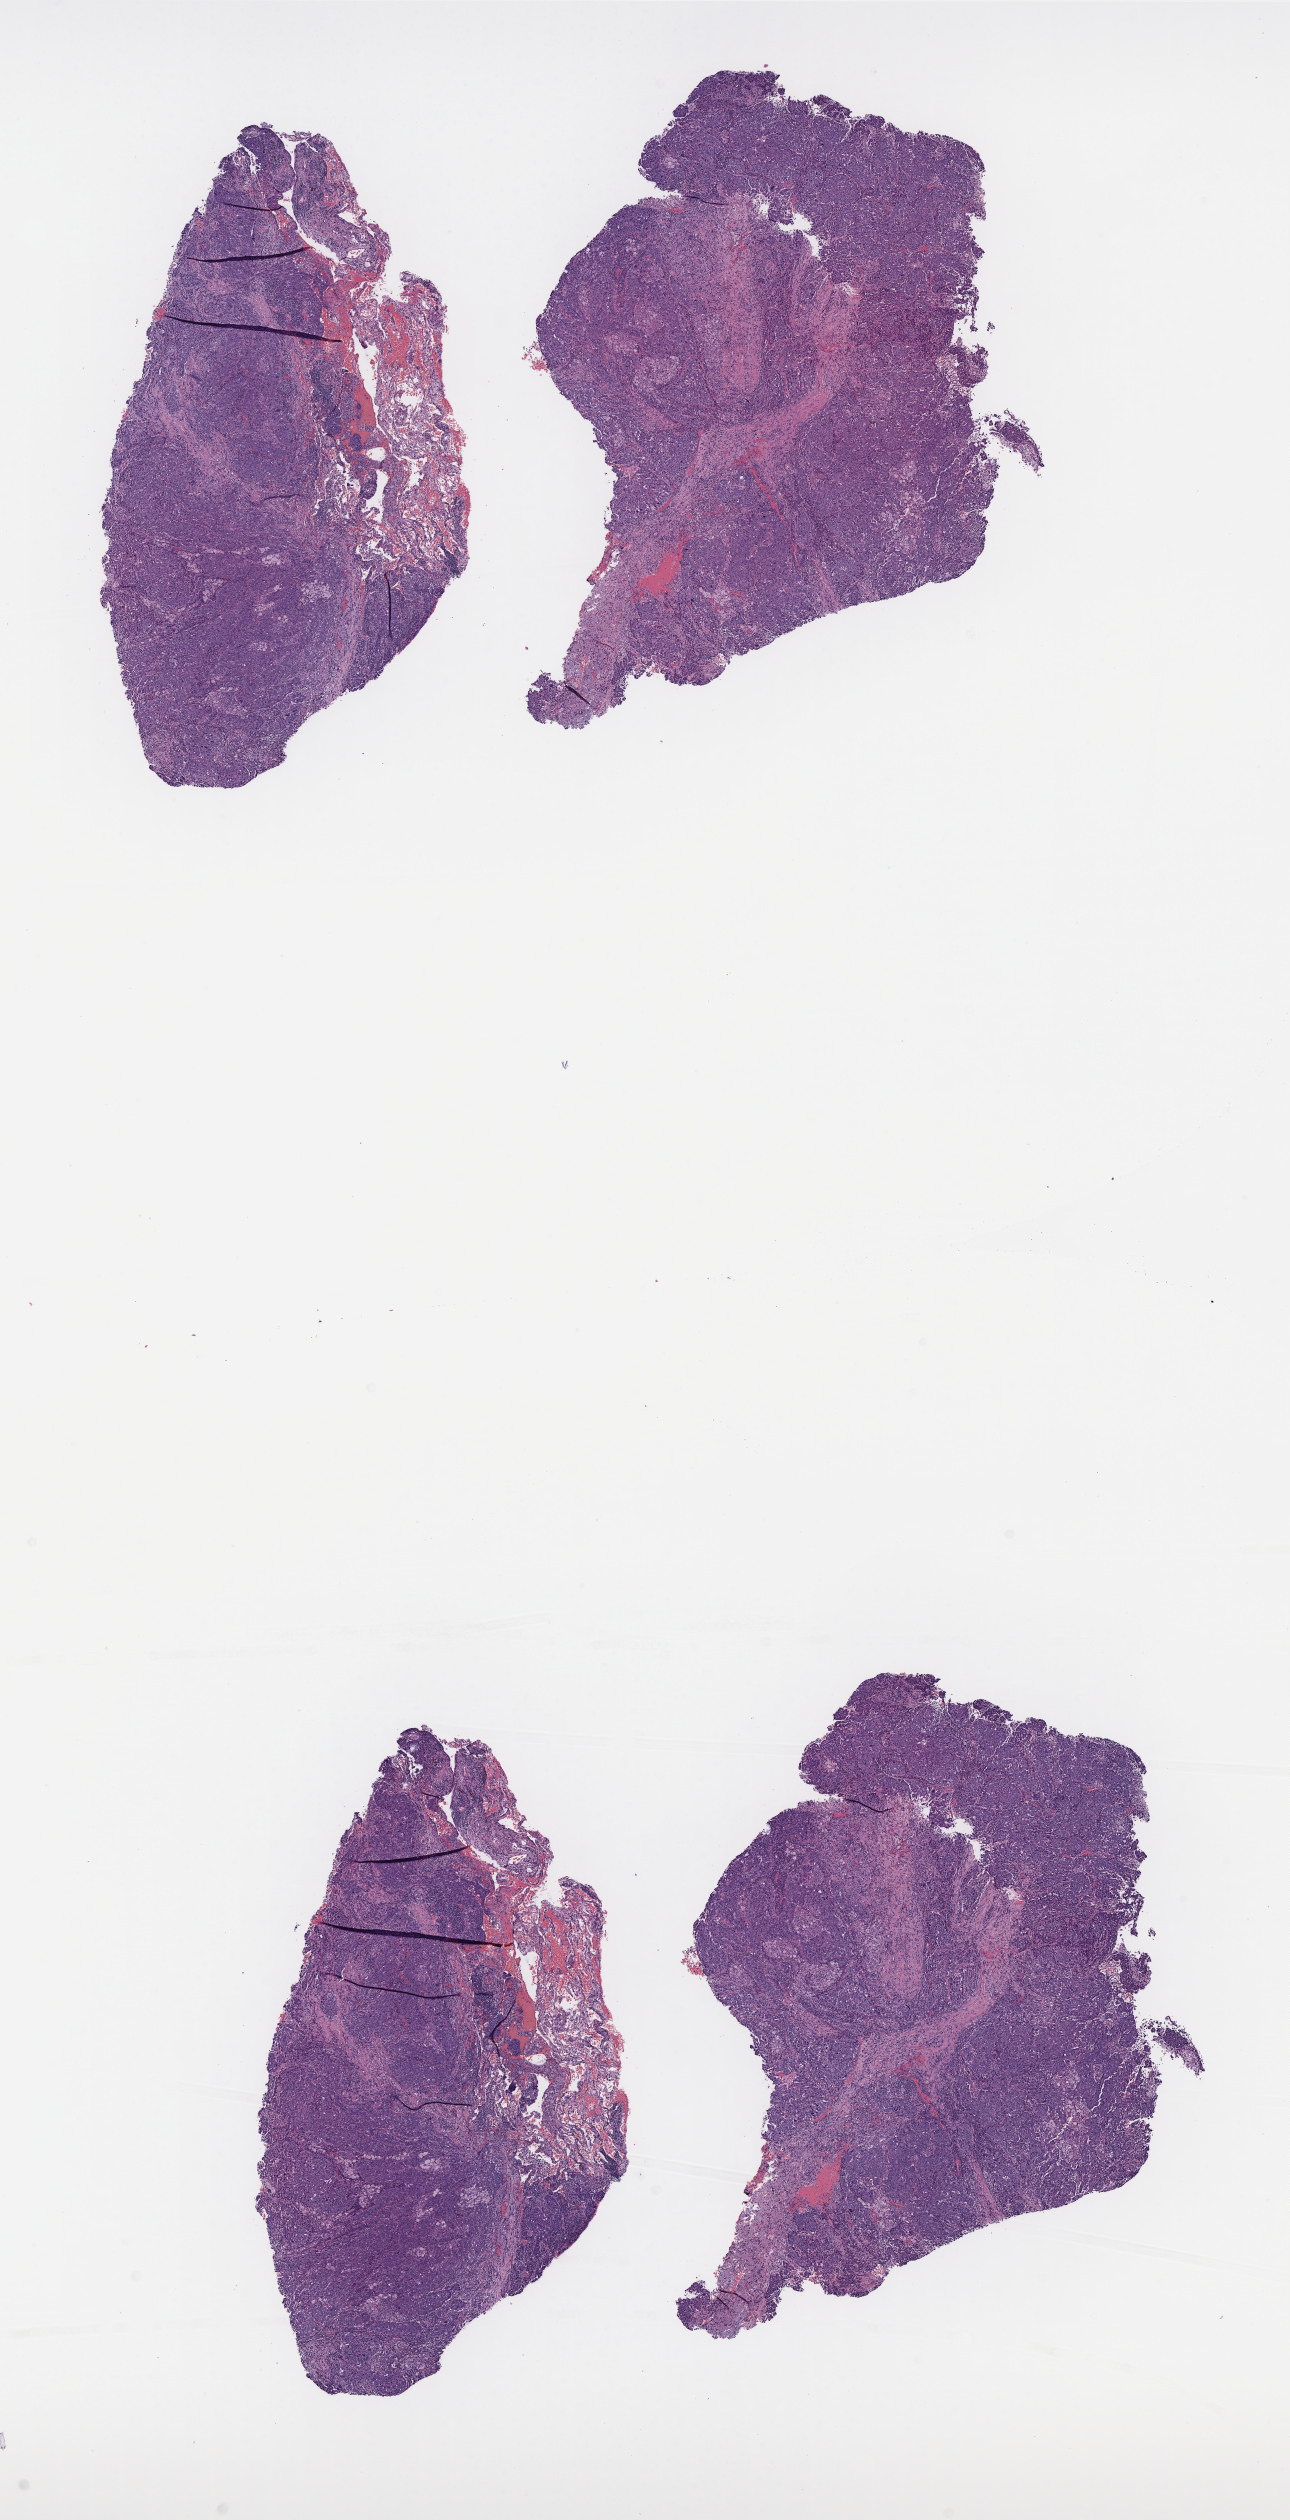
Digitized H&E-stained tissue section (whole slide) — a low-resolution overview of the entire scanned area, about 10.3 x 20.2 mm (from a 40x scan). Formalin-fixed paraffin-embedded (FFPE) diagnostic section. Lung, primary tumour sample. Patient: female, age at initial diagnosis 67 years.
Diagnosis: Squamous cell carcinoma, NOS. AJCC pathologic stage: IIB (7th edition). TNM: T3 N0 M0.